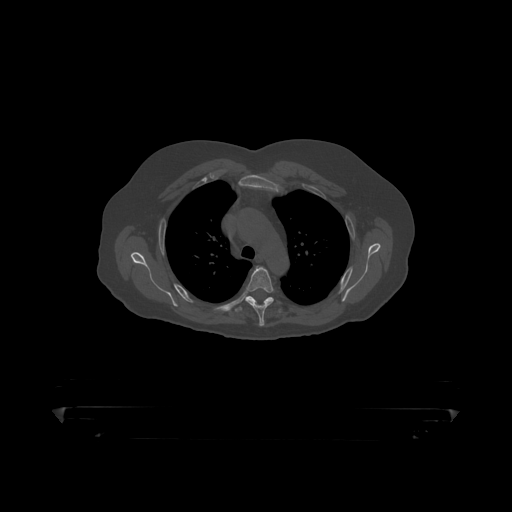
CT including the spine, one axial slice. Slice 334 of 390 in the series (ordered by position). Reconstruction kernel STANDARD. Bone window (W 1800 / L 400 HU). 512 × 512 image matrix, field of view 650 × 650 mm. Male patient, age 60 years. Case-level facts recorded for this patient, not image findings: primary cancer: prostate.
Structures marked on this image (semi-automatically segmented with operator editing):
- T4 vertebra: bounding box [x1, y1, x2, y2] px = [245, 267, 275, 319]
- T5 vertebra: [235, 296, 284, 315]